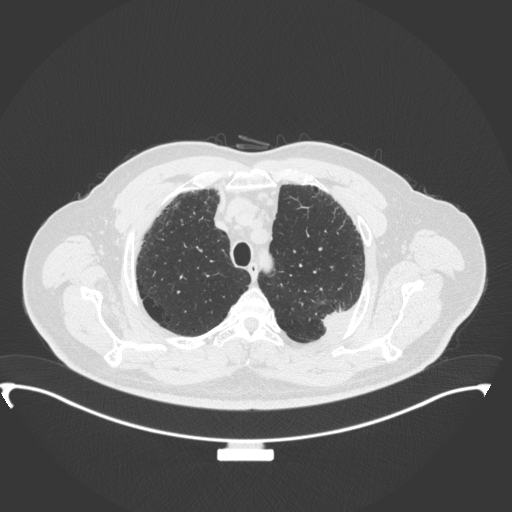
Chest CT, one axial slice. Position 293 of 350 along the scan axis. 120 kVp. Lung window (W 1500 / L -600 HU). 512 × 512 image matrix, field of view 459 × 459 mm. Patient: male, 64 years. From the clinical record (not read from this slice): clinical TNM (as recorded): T1c N1 M1.
Annotated regions visible in this slice (rectangle marked by the reading radiologist):
- lung tumour (recorded histology: adenocarcinoma): bounding box <318,305,346,331> (left, top, right, bottom; pixels)